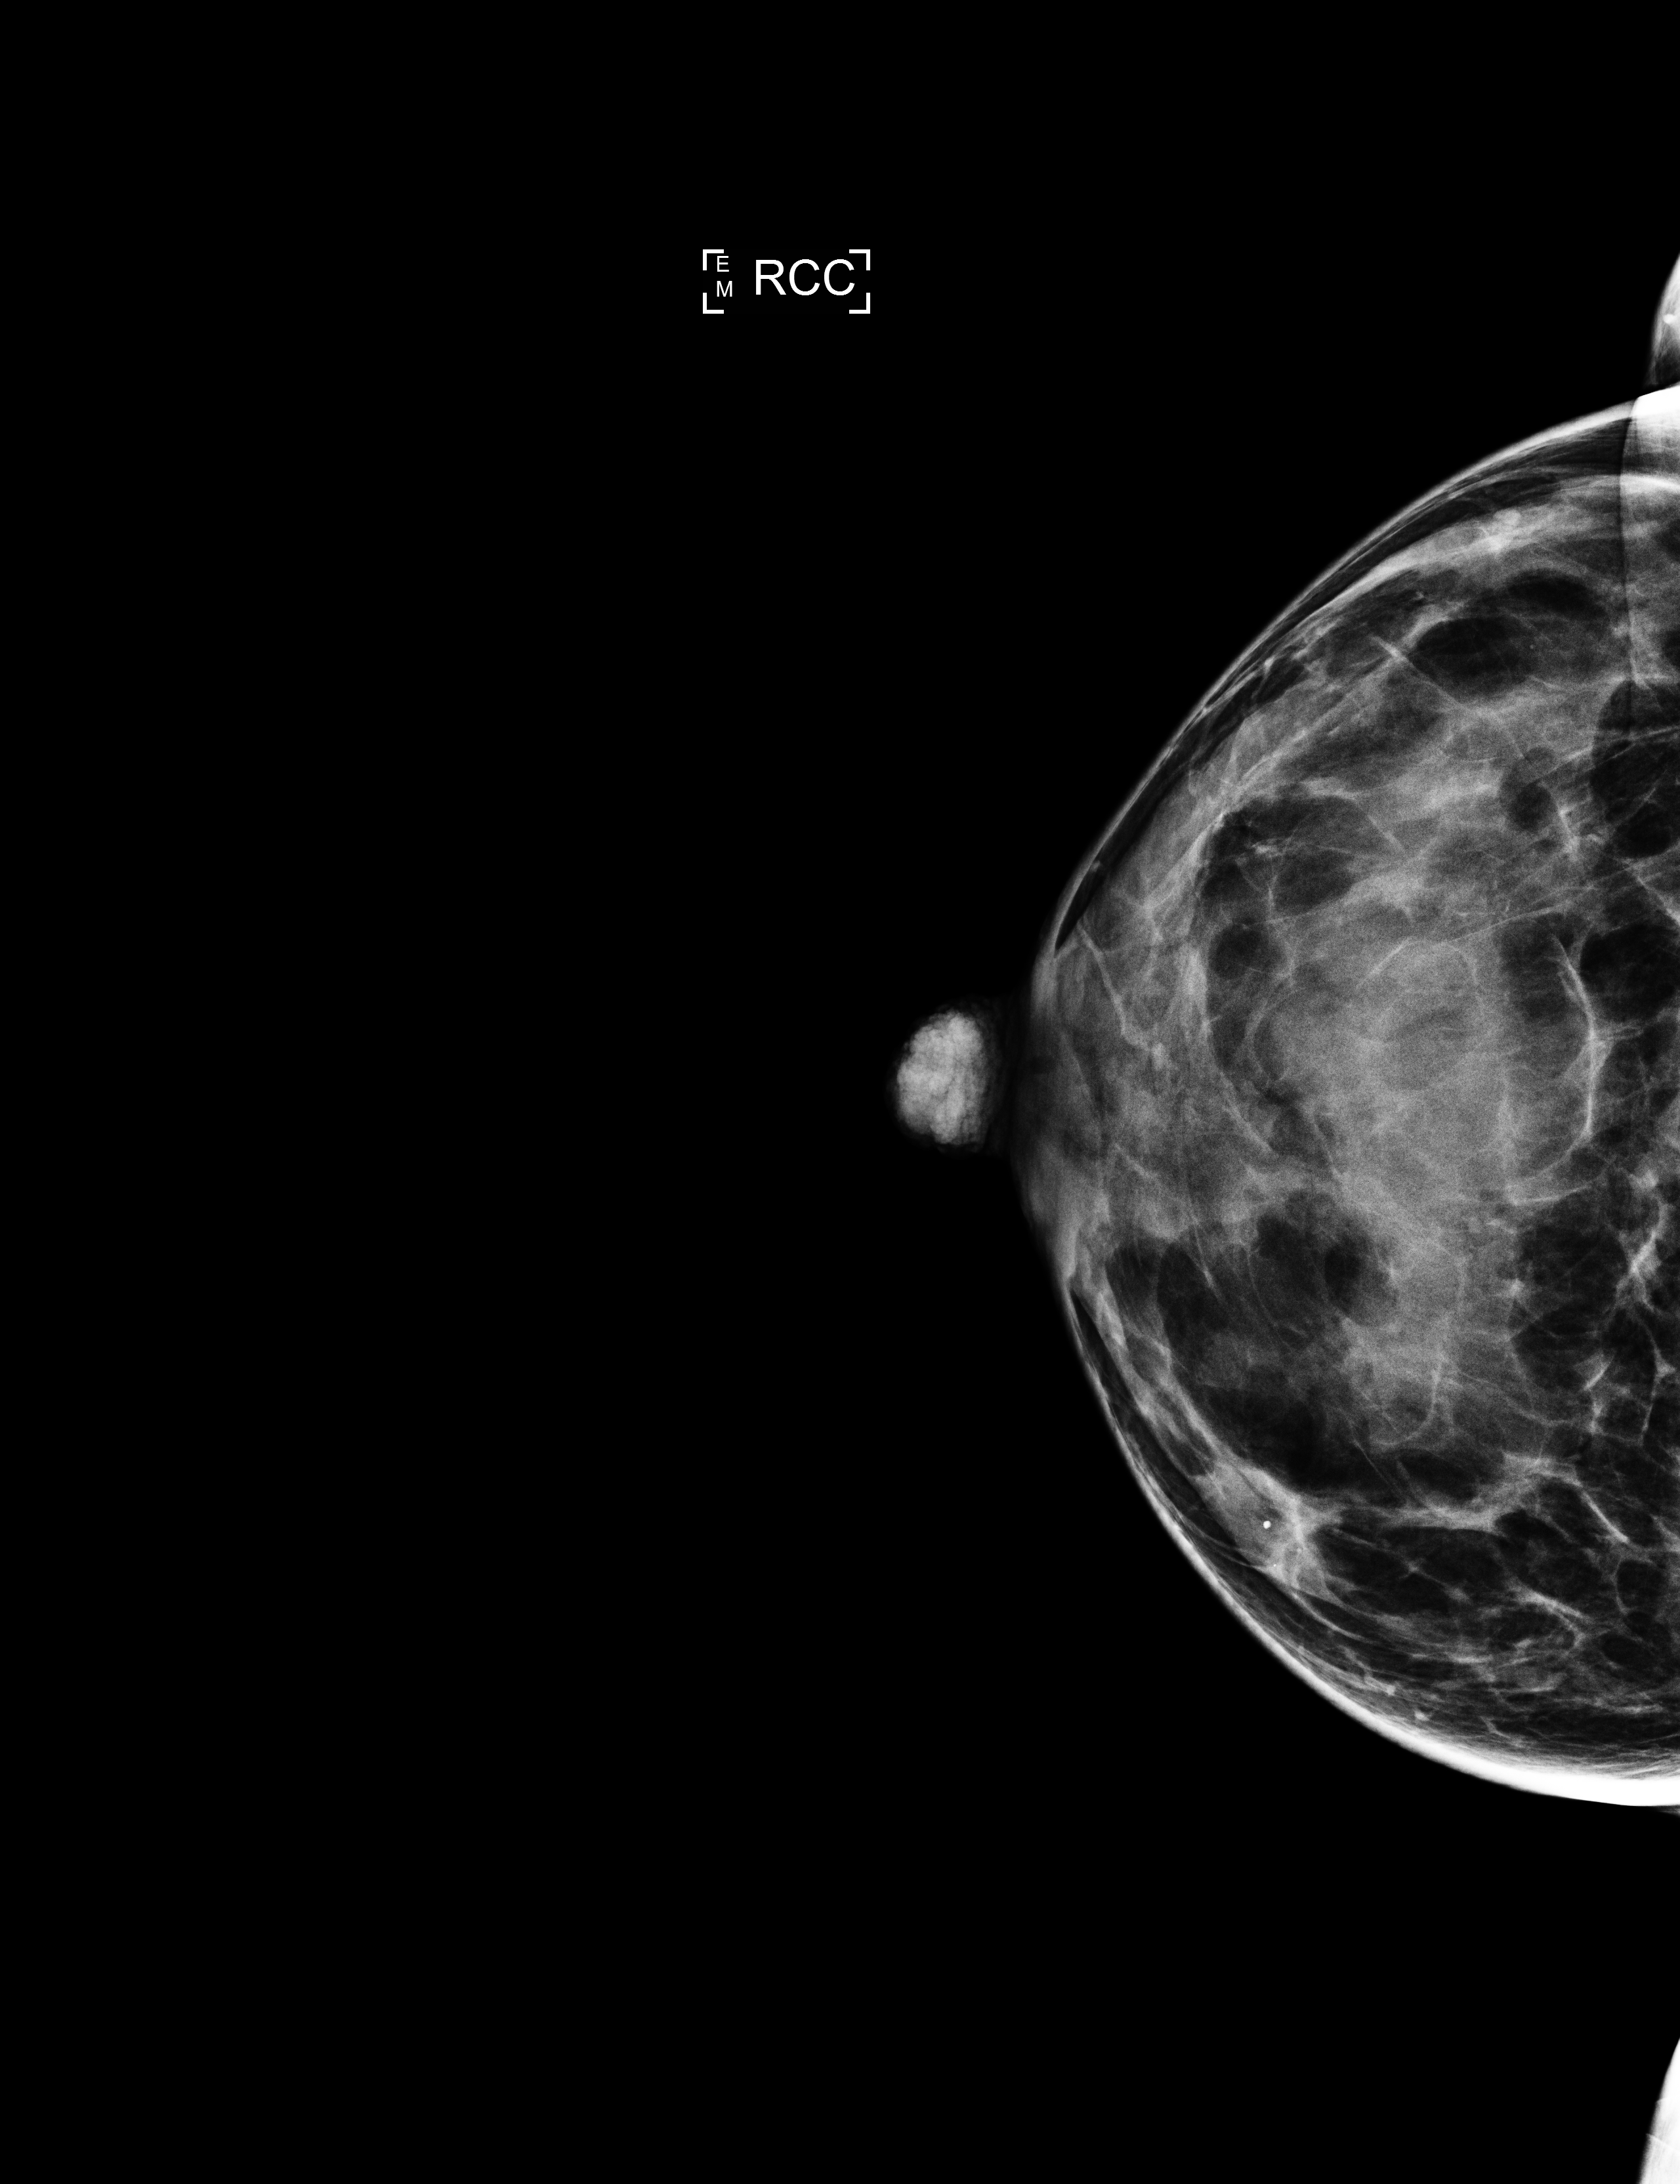
Screening examination, compressed breast thickness 37 mm, system: Selenia Dimensions. Patient: female, 43 years.
Image type: full-field digital mammogram. Breast: right. Projection: craniocaudal (CC) view.